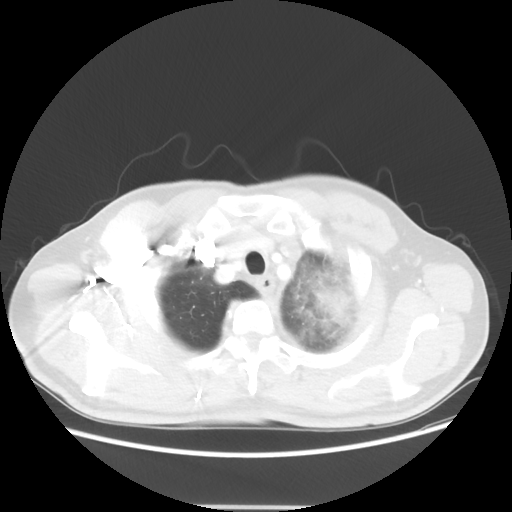
Chest CT, one axial slice. Slice 50 of 53 in the series (ordered by position). Lung window (W 1500 / L -600 HU). 512 × 512 image matrix, field of view 391 × 391 mm. Patient: male, 60 years. From the clinical record (not read from this slice): clinical TNM (as recorded): T4 N1 M1a.
Annotated regions visible in this slice (rectangle marked by the reading radiologist):
- lung tumour (recorded histology: large cell carcinoma): bounding box (x1, y1, x2, y2) in pixels: (305, 272, 364, 339)